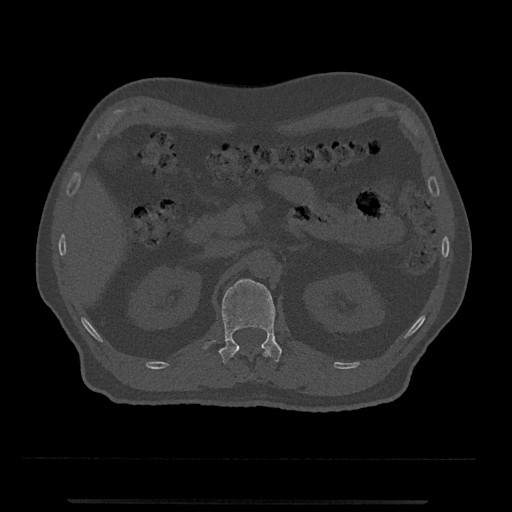
CT including the spine, one axial slice; position 352 of 797 along the scan axis; 120 kVp; bone window (W 1800 / L 400 HU); 512 × 512 image matrix, field of view 419 × 419 mm. Patient: male, 63 years. From the clinical record (not read from this slice): primary cancer: prostate.
Annotated regions visible in this slice (semi-automatically segmented with operator editing):
- L1 vertebra: box from (x=204, y=279) to (x=282, y=365) px
- T12 vertebra: (x=233, y=348)–(x=269, y=358)